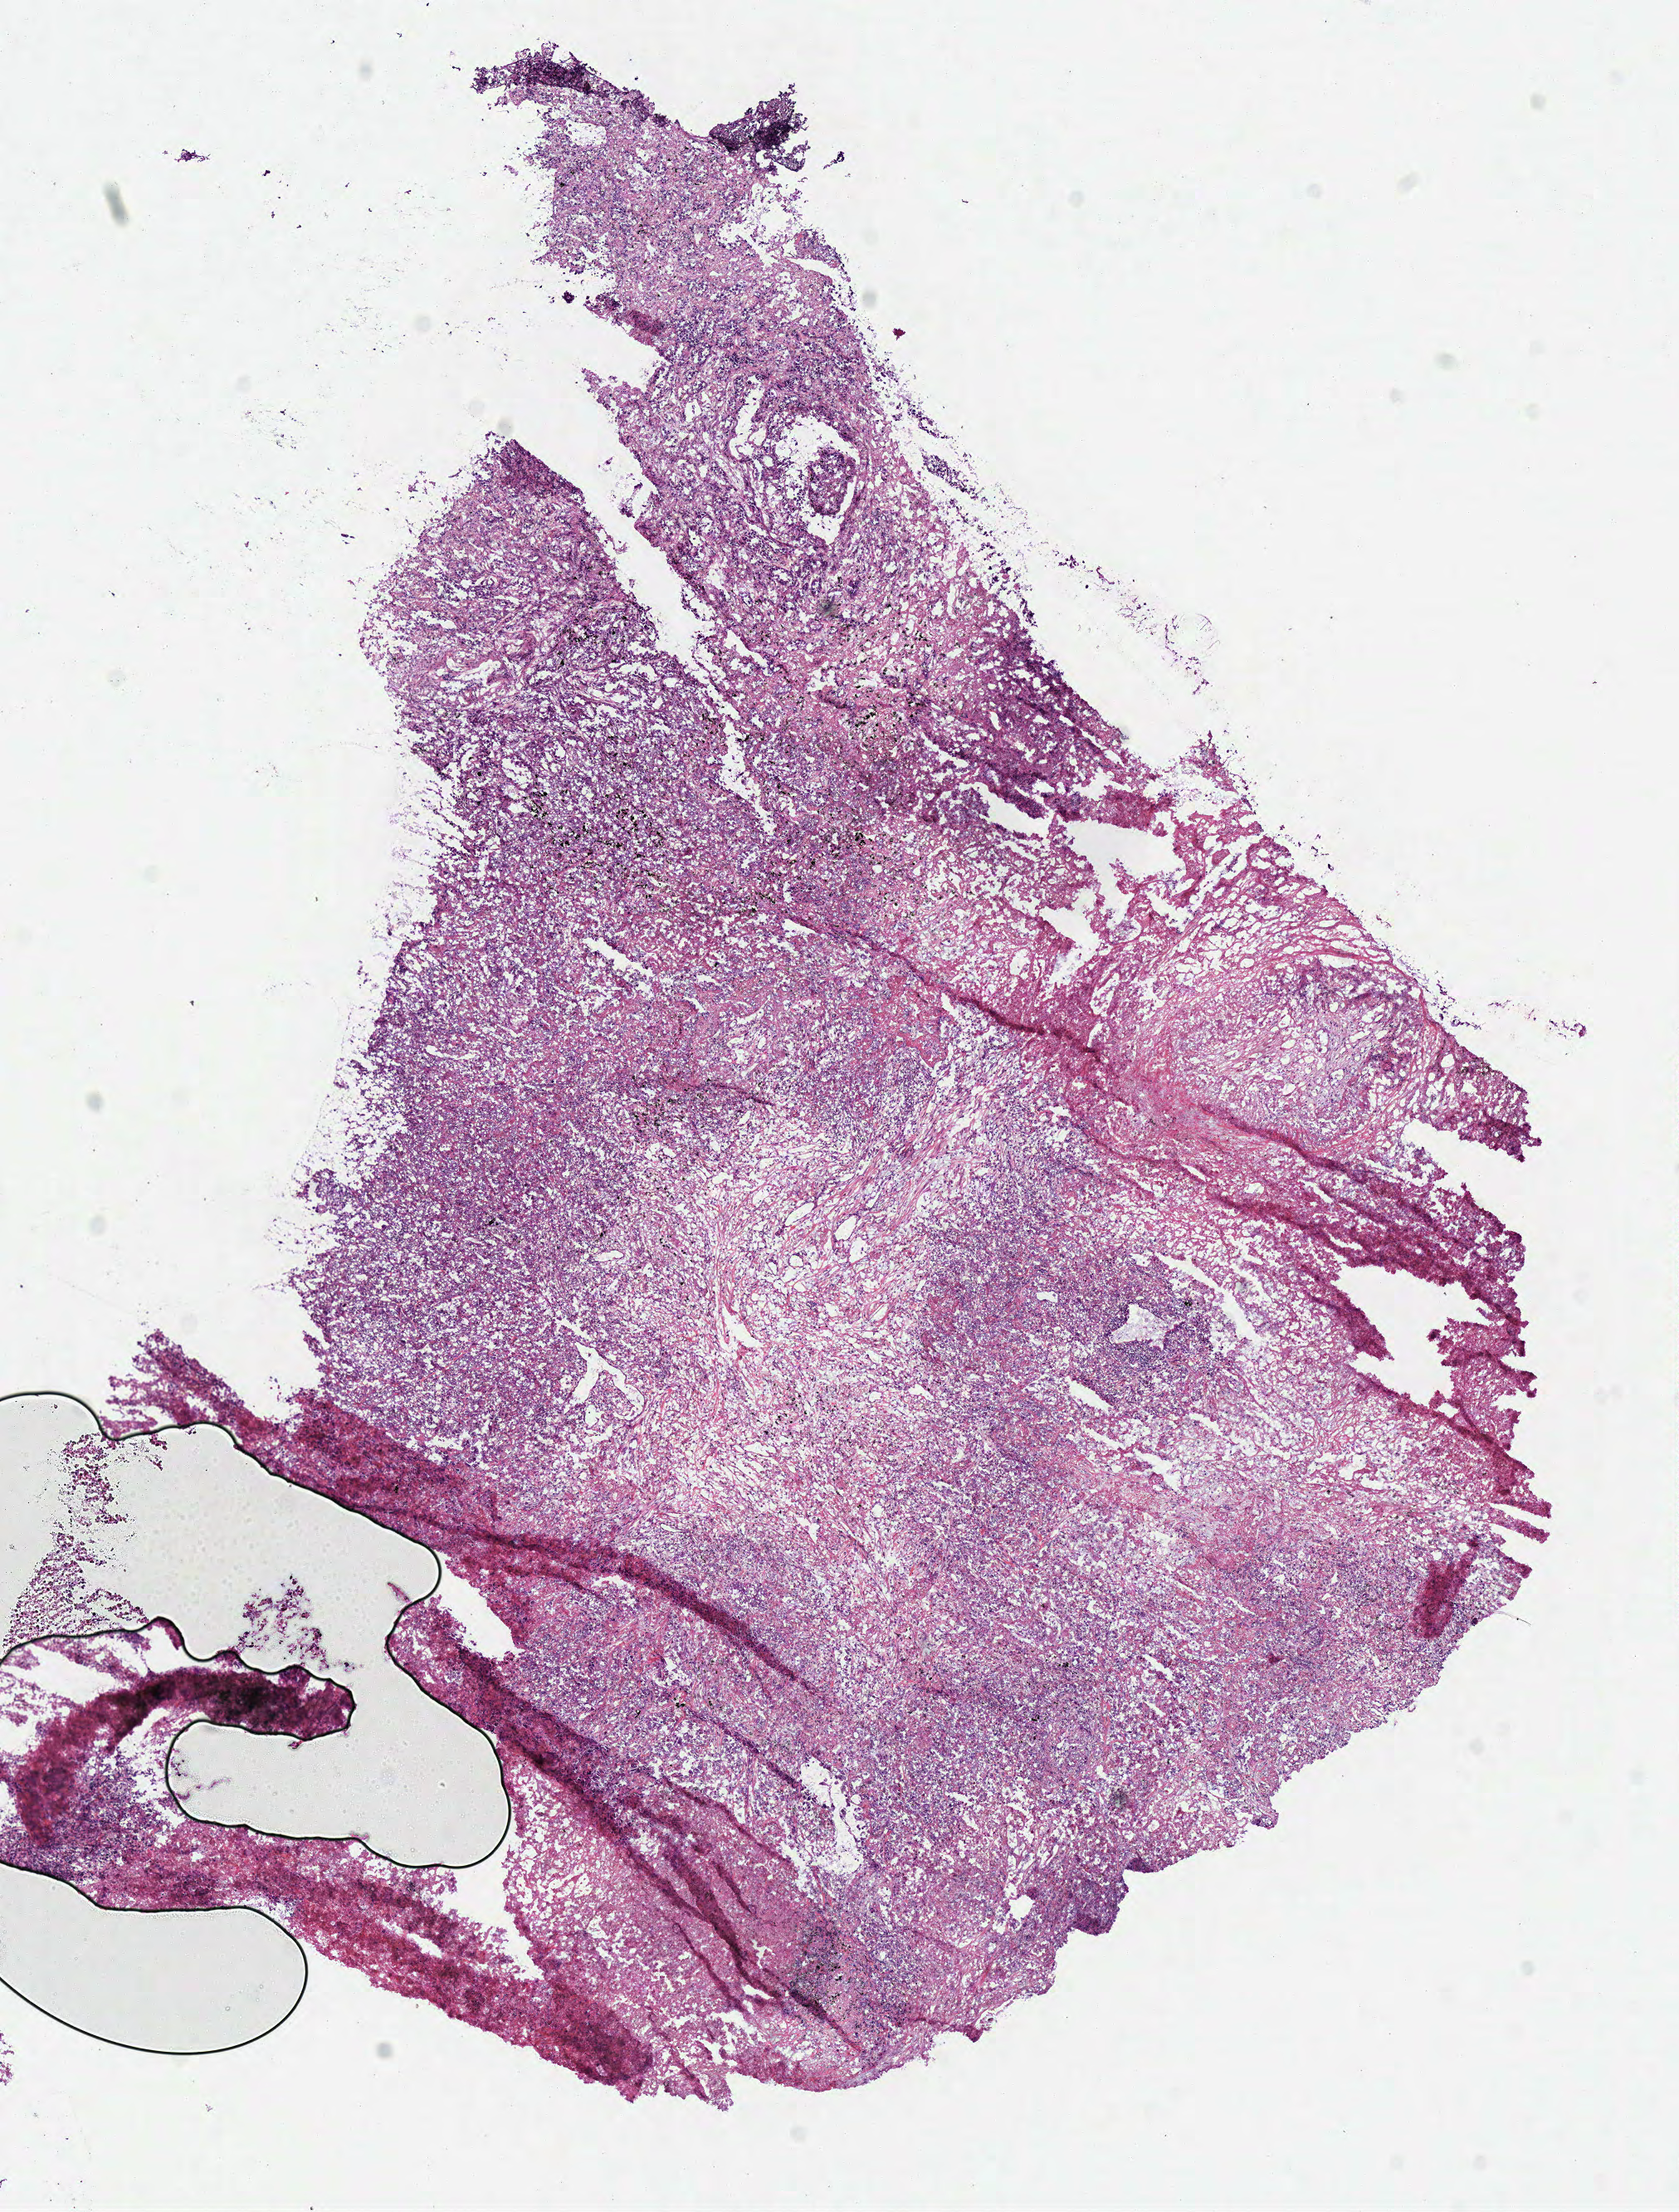
Digitized H&E tissue section (whole slide), shown as a low-resolution overview of the whole scanned area (about 8.0 x 10.5 mm, from a 40x scan). Frozen section. Sample: primary tumour, lung. Female, age 74 years at initial diagnosis. Slide review estimates, as recorded: tumour cells 80%, tumour nuclei 80%, normal cells 0%, stromal cells 10%, necrosis 10%.
- pathologic diagnosis: Adenocarcinoma, NOS
- AJCC pathologic stage: IIIA
- TNM: T2 N2 M0